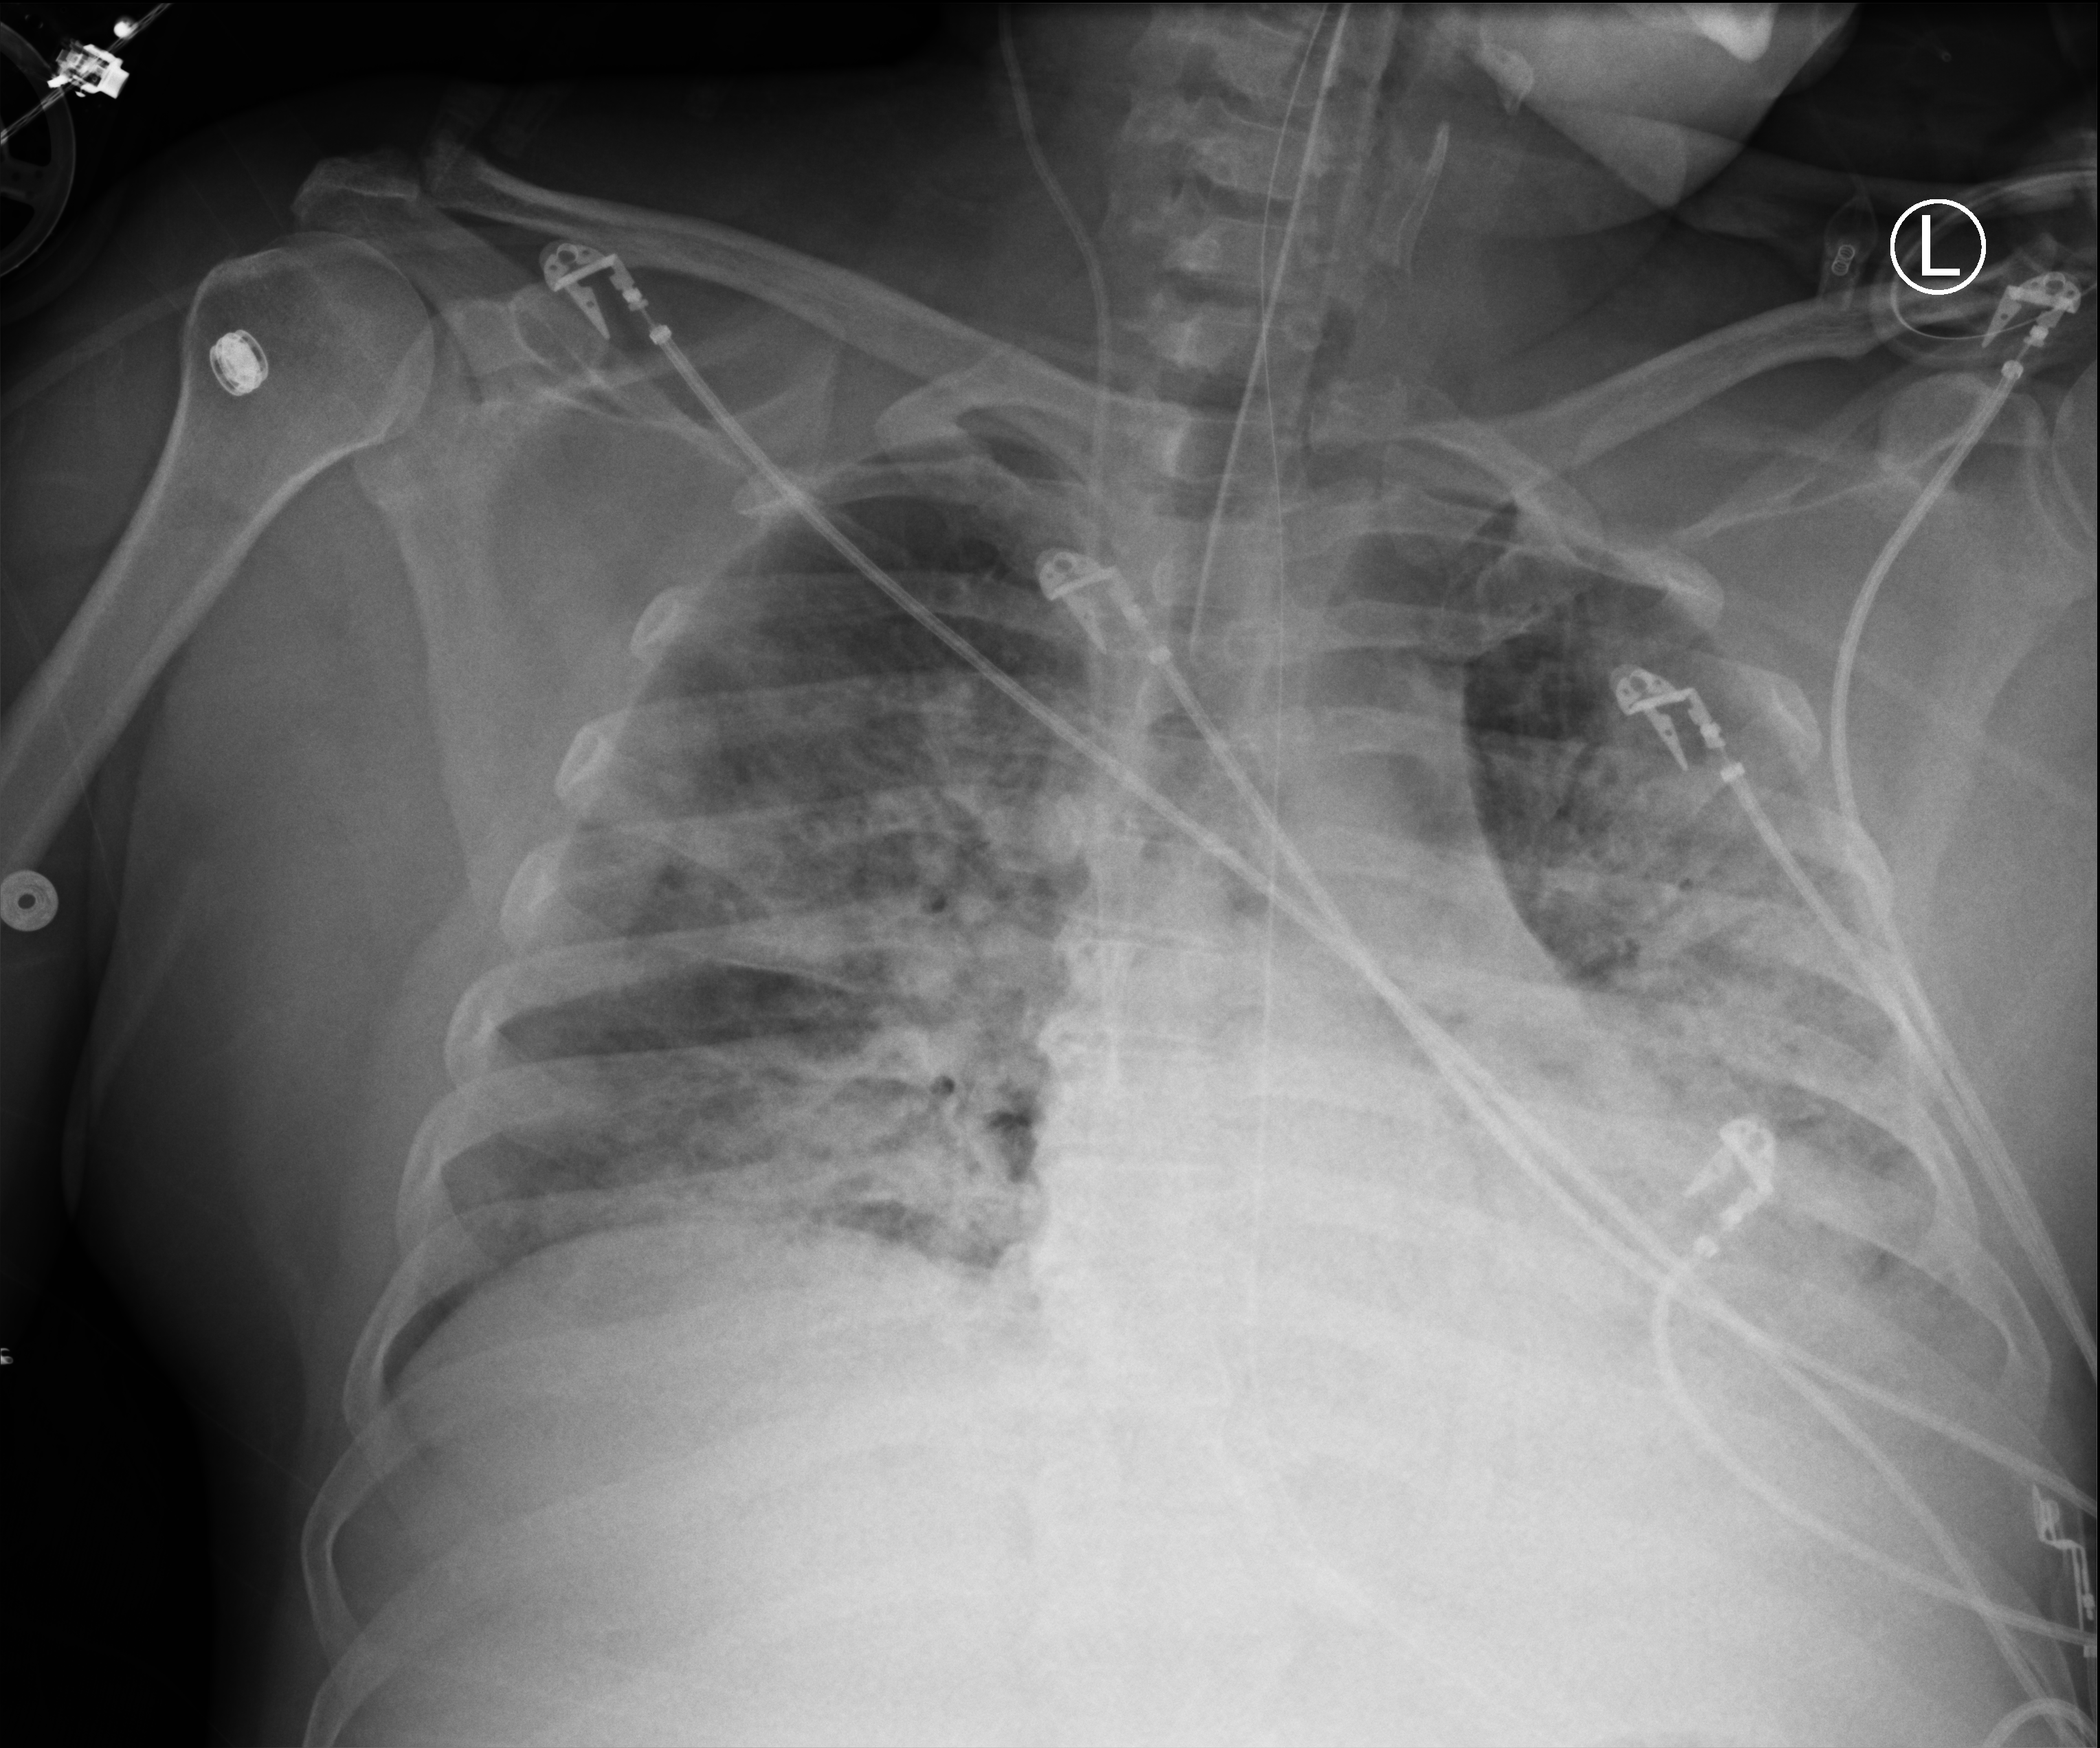
Portable chest radiograph, anteroposterior (AP) projection. Male patient hospitalised with COVID-19, age 18–59 years.
Admission-level facts for this patient (not findings on this image; timing relative to this image not recorded): admitted to intensive care during this hospital stay: yes; mechanically ventilated during this hospital stay: yes.